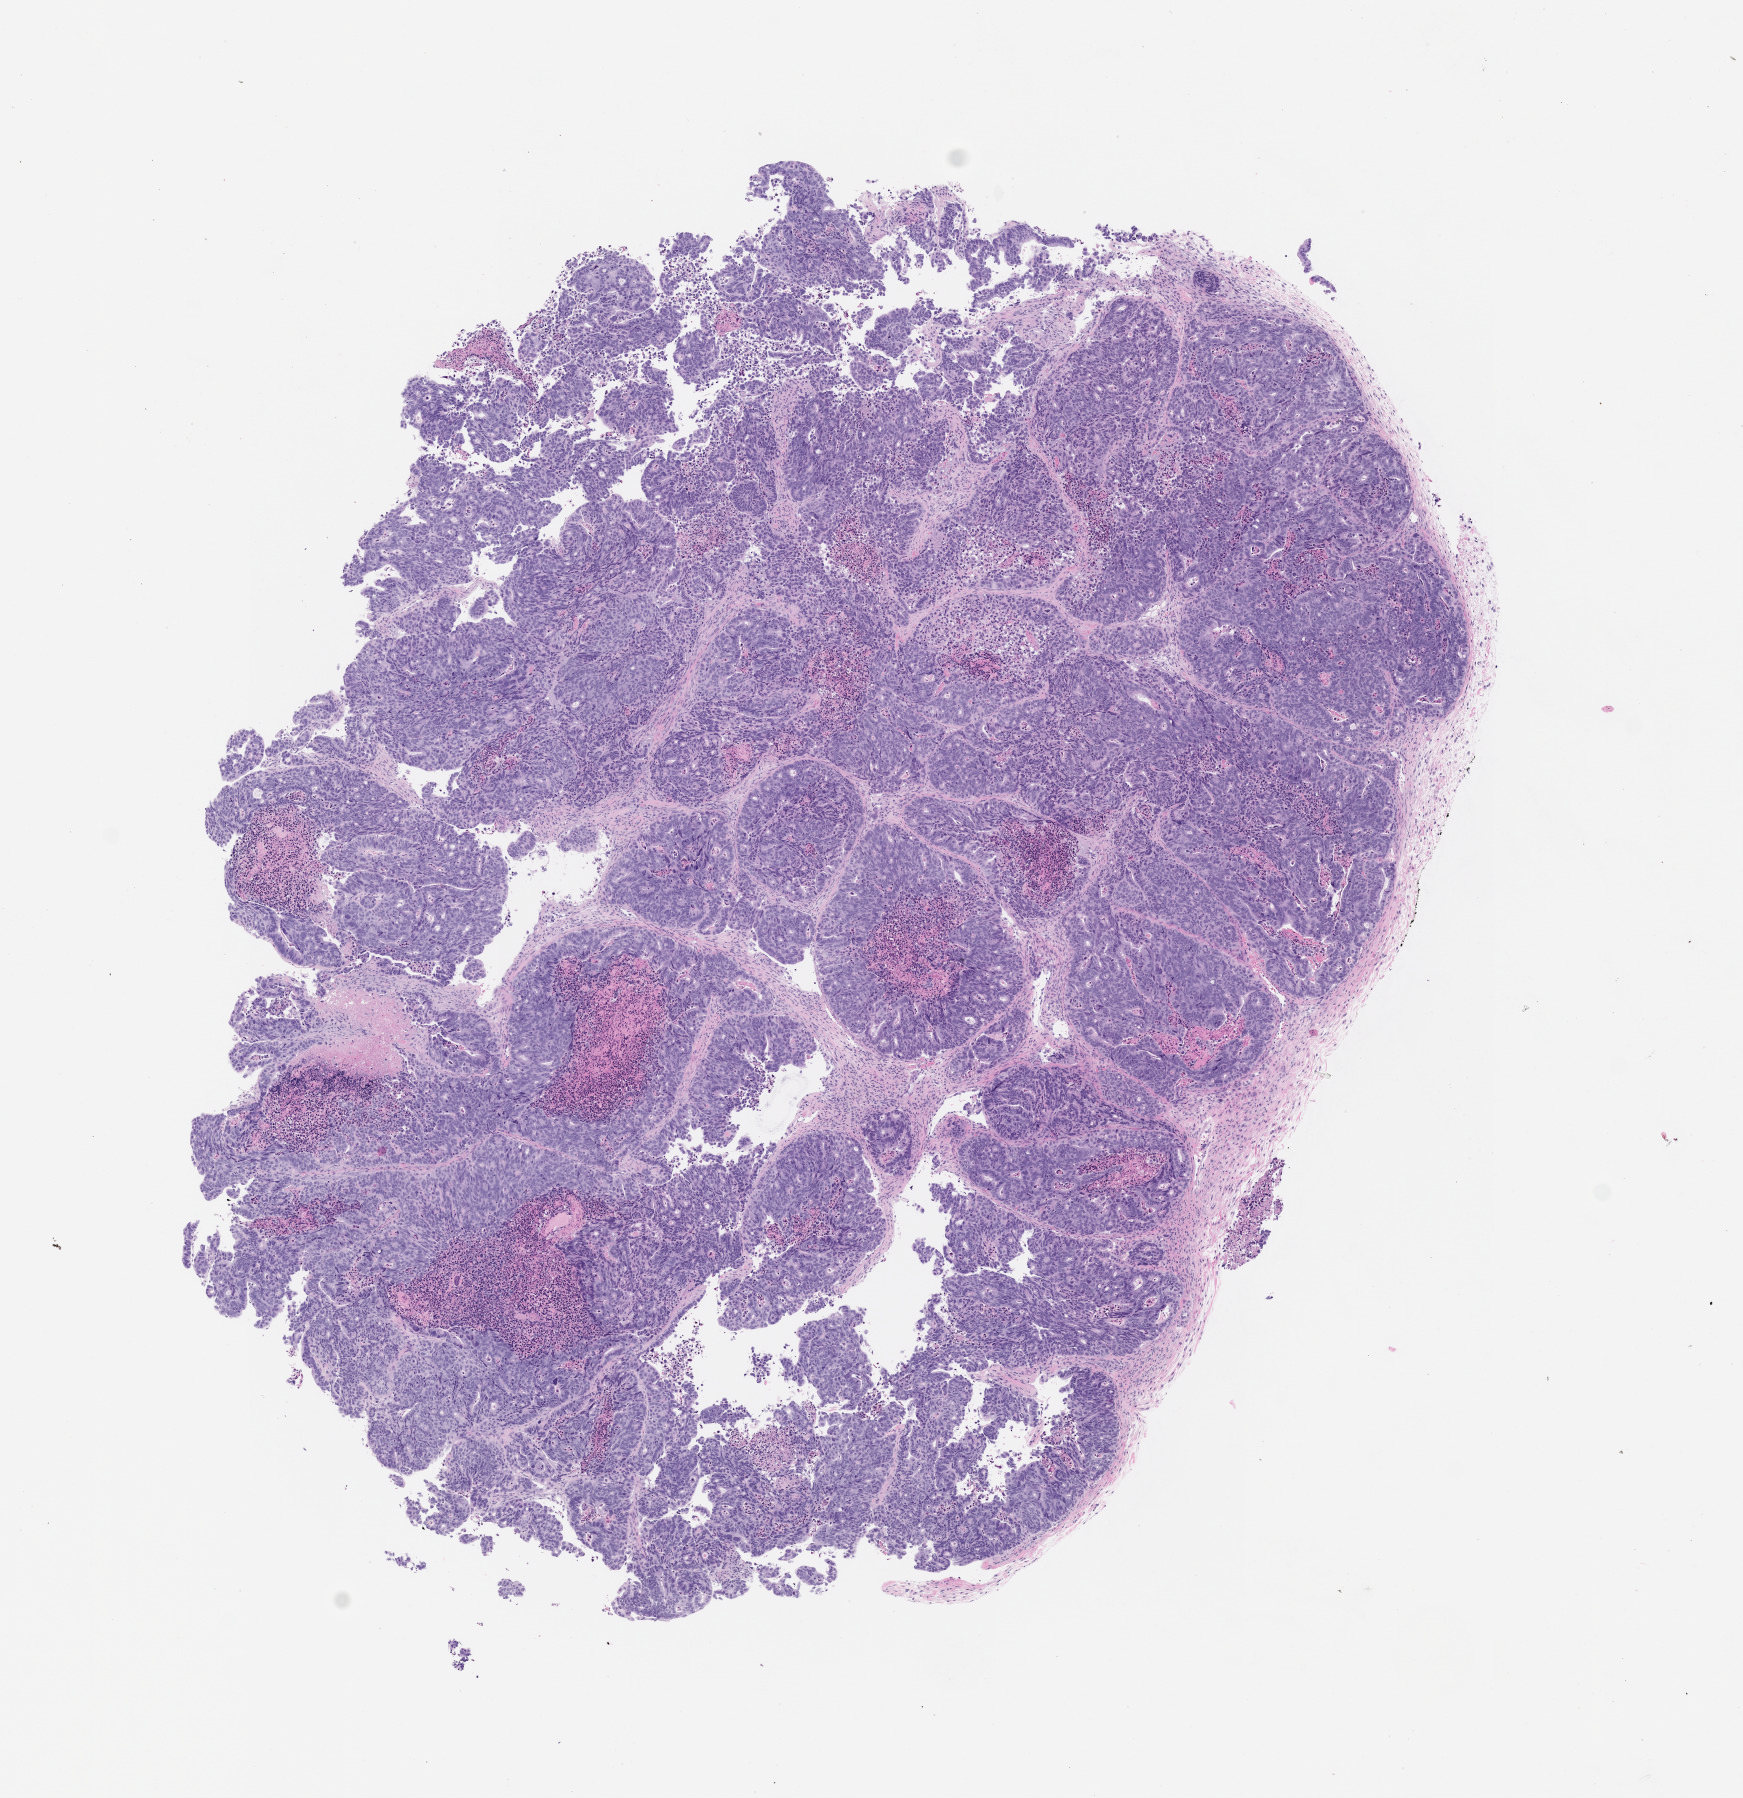
Whole-slide image, hematoxylin and eosin (H&E): patient-derived xenograft (human tumor grown in a mouse), passage 1, shown as a low-resolution overview of the whole scanned area (about 7.0 x 7.2 mm), formalin-fixed paraffin-embedded section, tumor site category: colon.
• originating patient diagnosis: Colon Adenocarcinoma